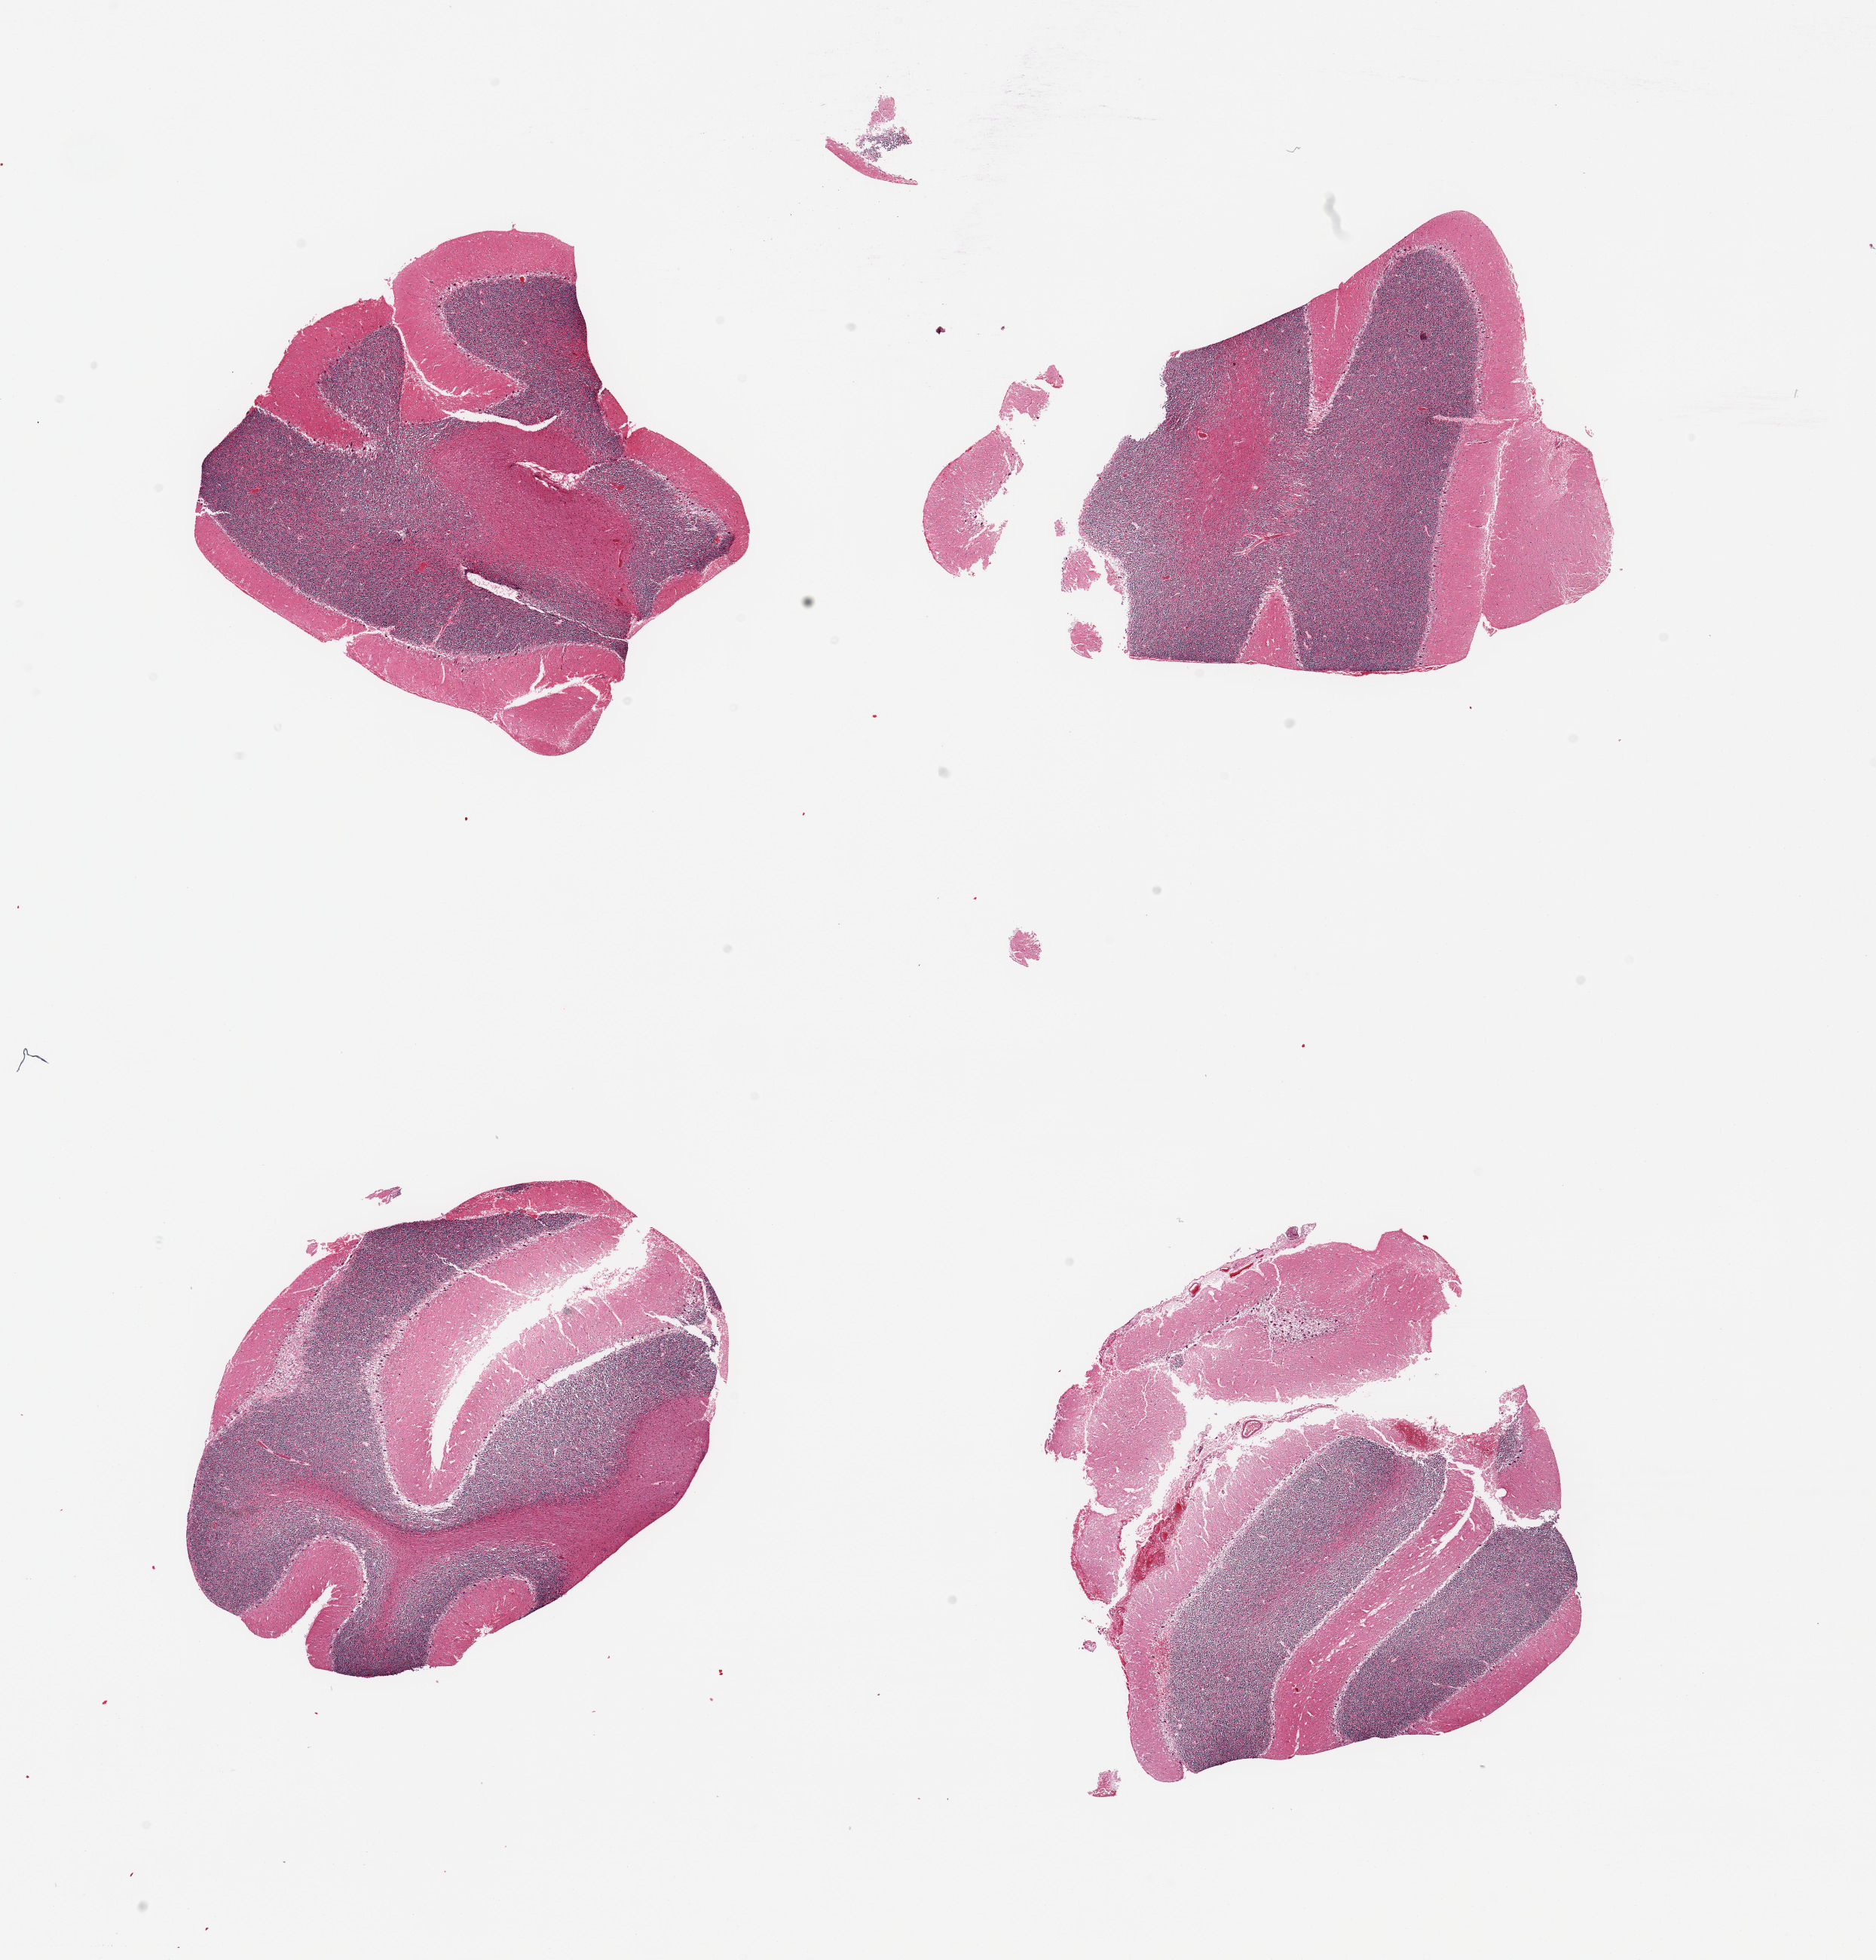
Haematoxylin and eosin whole-slide image, brightfield — a low-resolution overview of the entire scanned area, about 19.7 x 20.6 mm; PAXgene-fixed, paraffin-embedded tissue; sampled site (target tissue): cerebellum; tissue donor sample. Male donor.
- reviewer comment on this tissue sample: 4 pieces, no abnnormalities